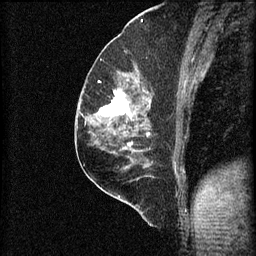
Breast MRI (dynamic contrast-enhanced), one sagittal slice. Position 35 of 60 along the scan axis. 3 images stored at this slice position (order not interpretable as contrast timing). 1.5 T. TE 4.2 ms, TR 8.2 ms. 256 × 256 image matrix, field of view 180 × 180 mm. Patient: female, 59 years.
Structures marked on this image (semi-automatic segmentation, software-assisted and operator-edited):
- analysis volume of interest (the breast-tissue region the enhancement analysis was run in; not a lesion): box from (x=92, y=74) to (x=155, y=131) px
- tumour enhancement mask (voxels above the 70 % enhancement threshold inside the analysis volume of interest): (x=99, y=82)–(x=152, y=117)